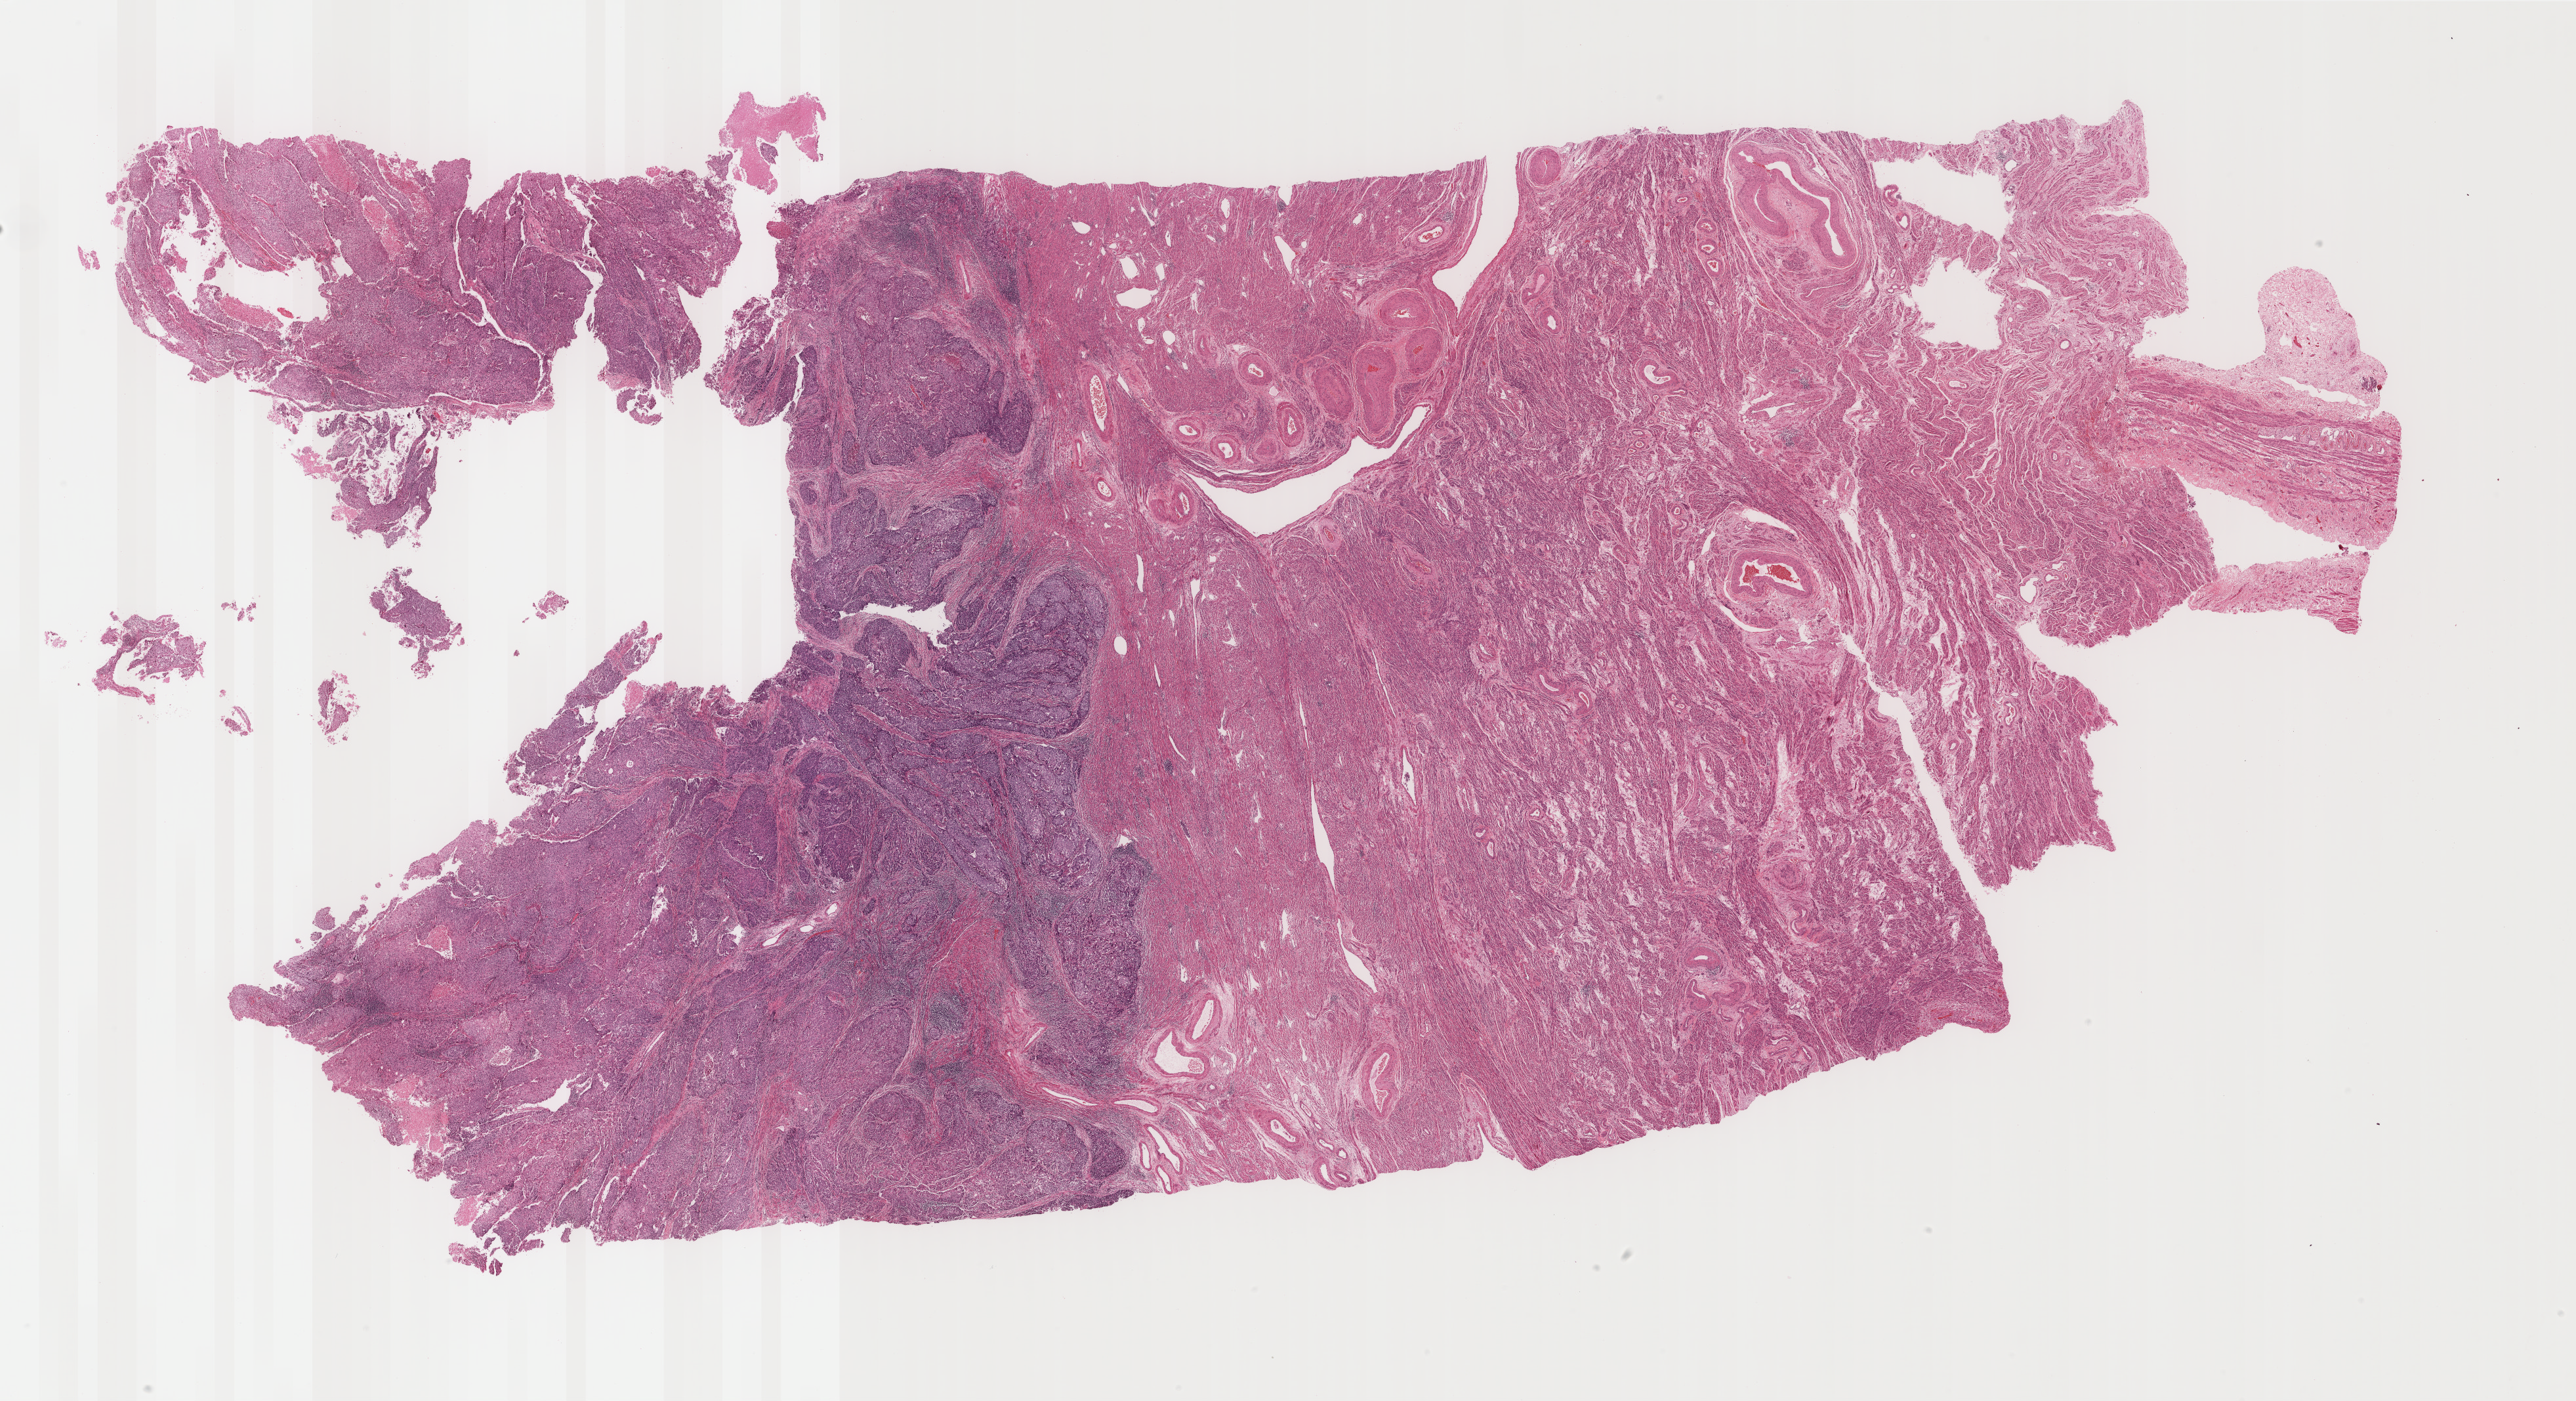
Whole-slide histology image, H&E, a low-resolution overview of the entire scanned area, about 31.2 x 16.9 mm. Formalin-fixed paraffin-embedded (FFPE) diagnostic section. Primary tumour sample from the uterus. Patient: female, age at initial diagnosis 60 years.
Histologic diagnosis: Endometrioid adenocarcinoma, NOS (endometrium).